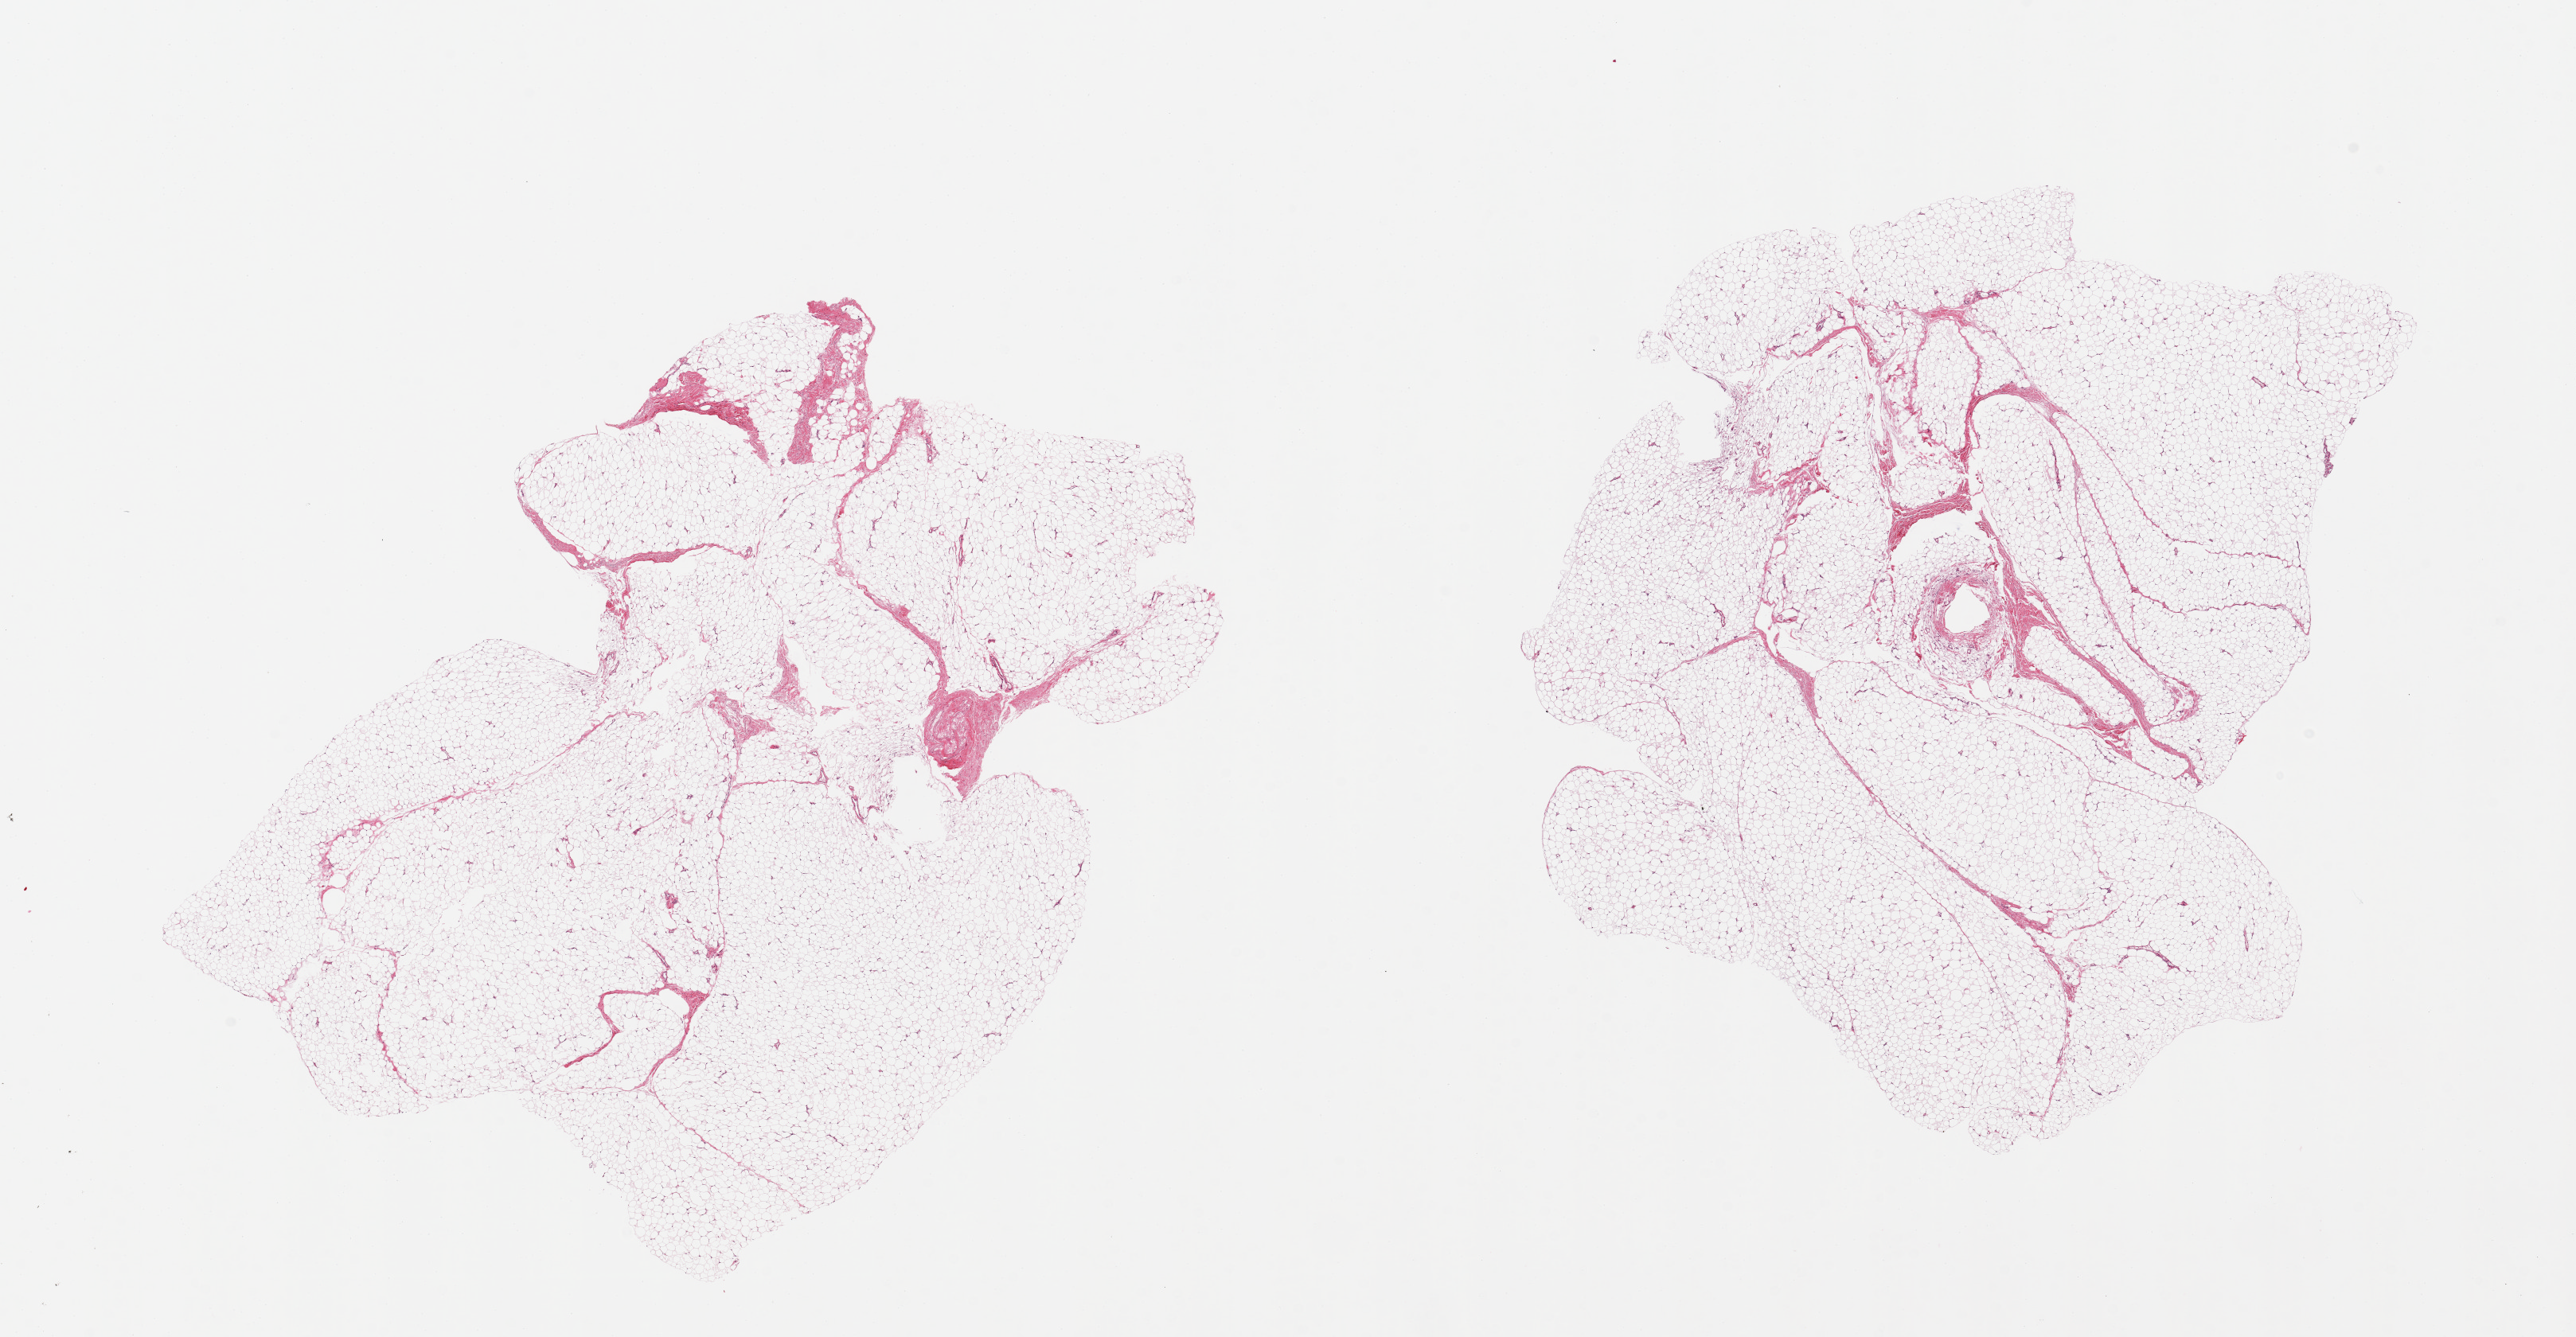
Whole-slide image, hematoxylin and eosin (H&E) stain — shown as a low-resolution overview of the whole scanned area (about 25.6 x 13.3 mm, slide scanned at 20x). PAXgene-fixed paraffin-embedded (PFPE) section. Sampled site (target tissue): adipose tissue. Donor tissue sample. Donor sex: male.
Pathologist's review note for this sample: 2 pieces, fascia elements up to ~10% of tissue.